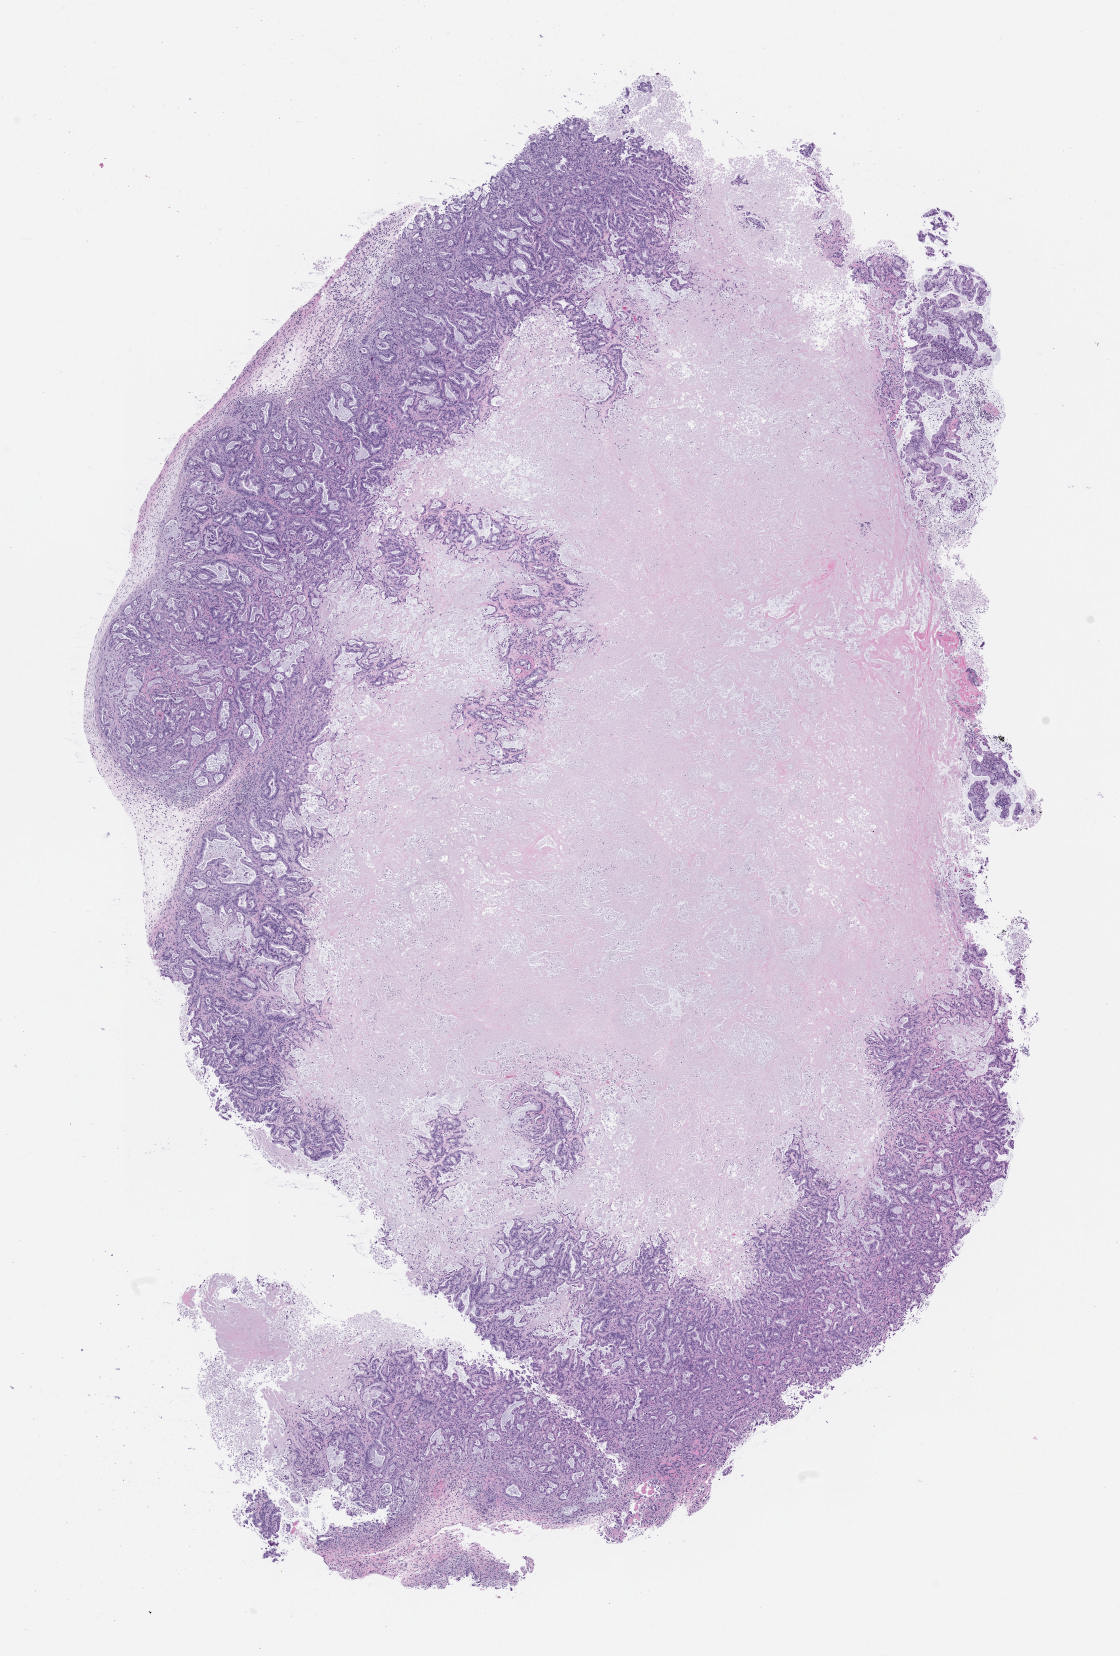
Whole-slide image, hematoxylin and eosin (H&E): patient-derived xenograft (human tumor grown in a mouse), passage 3 — low-resolution overview of the scanned area, about 9.0 x 13.3 mm, formalin-fixed, paraffin-embedded (FFPE) tissue, originating tumor site category: pancreas.
- originating patient diagnosis: Pancreatic Adenocarcinoma